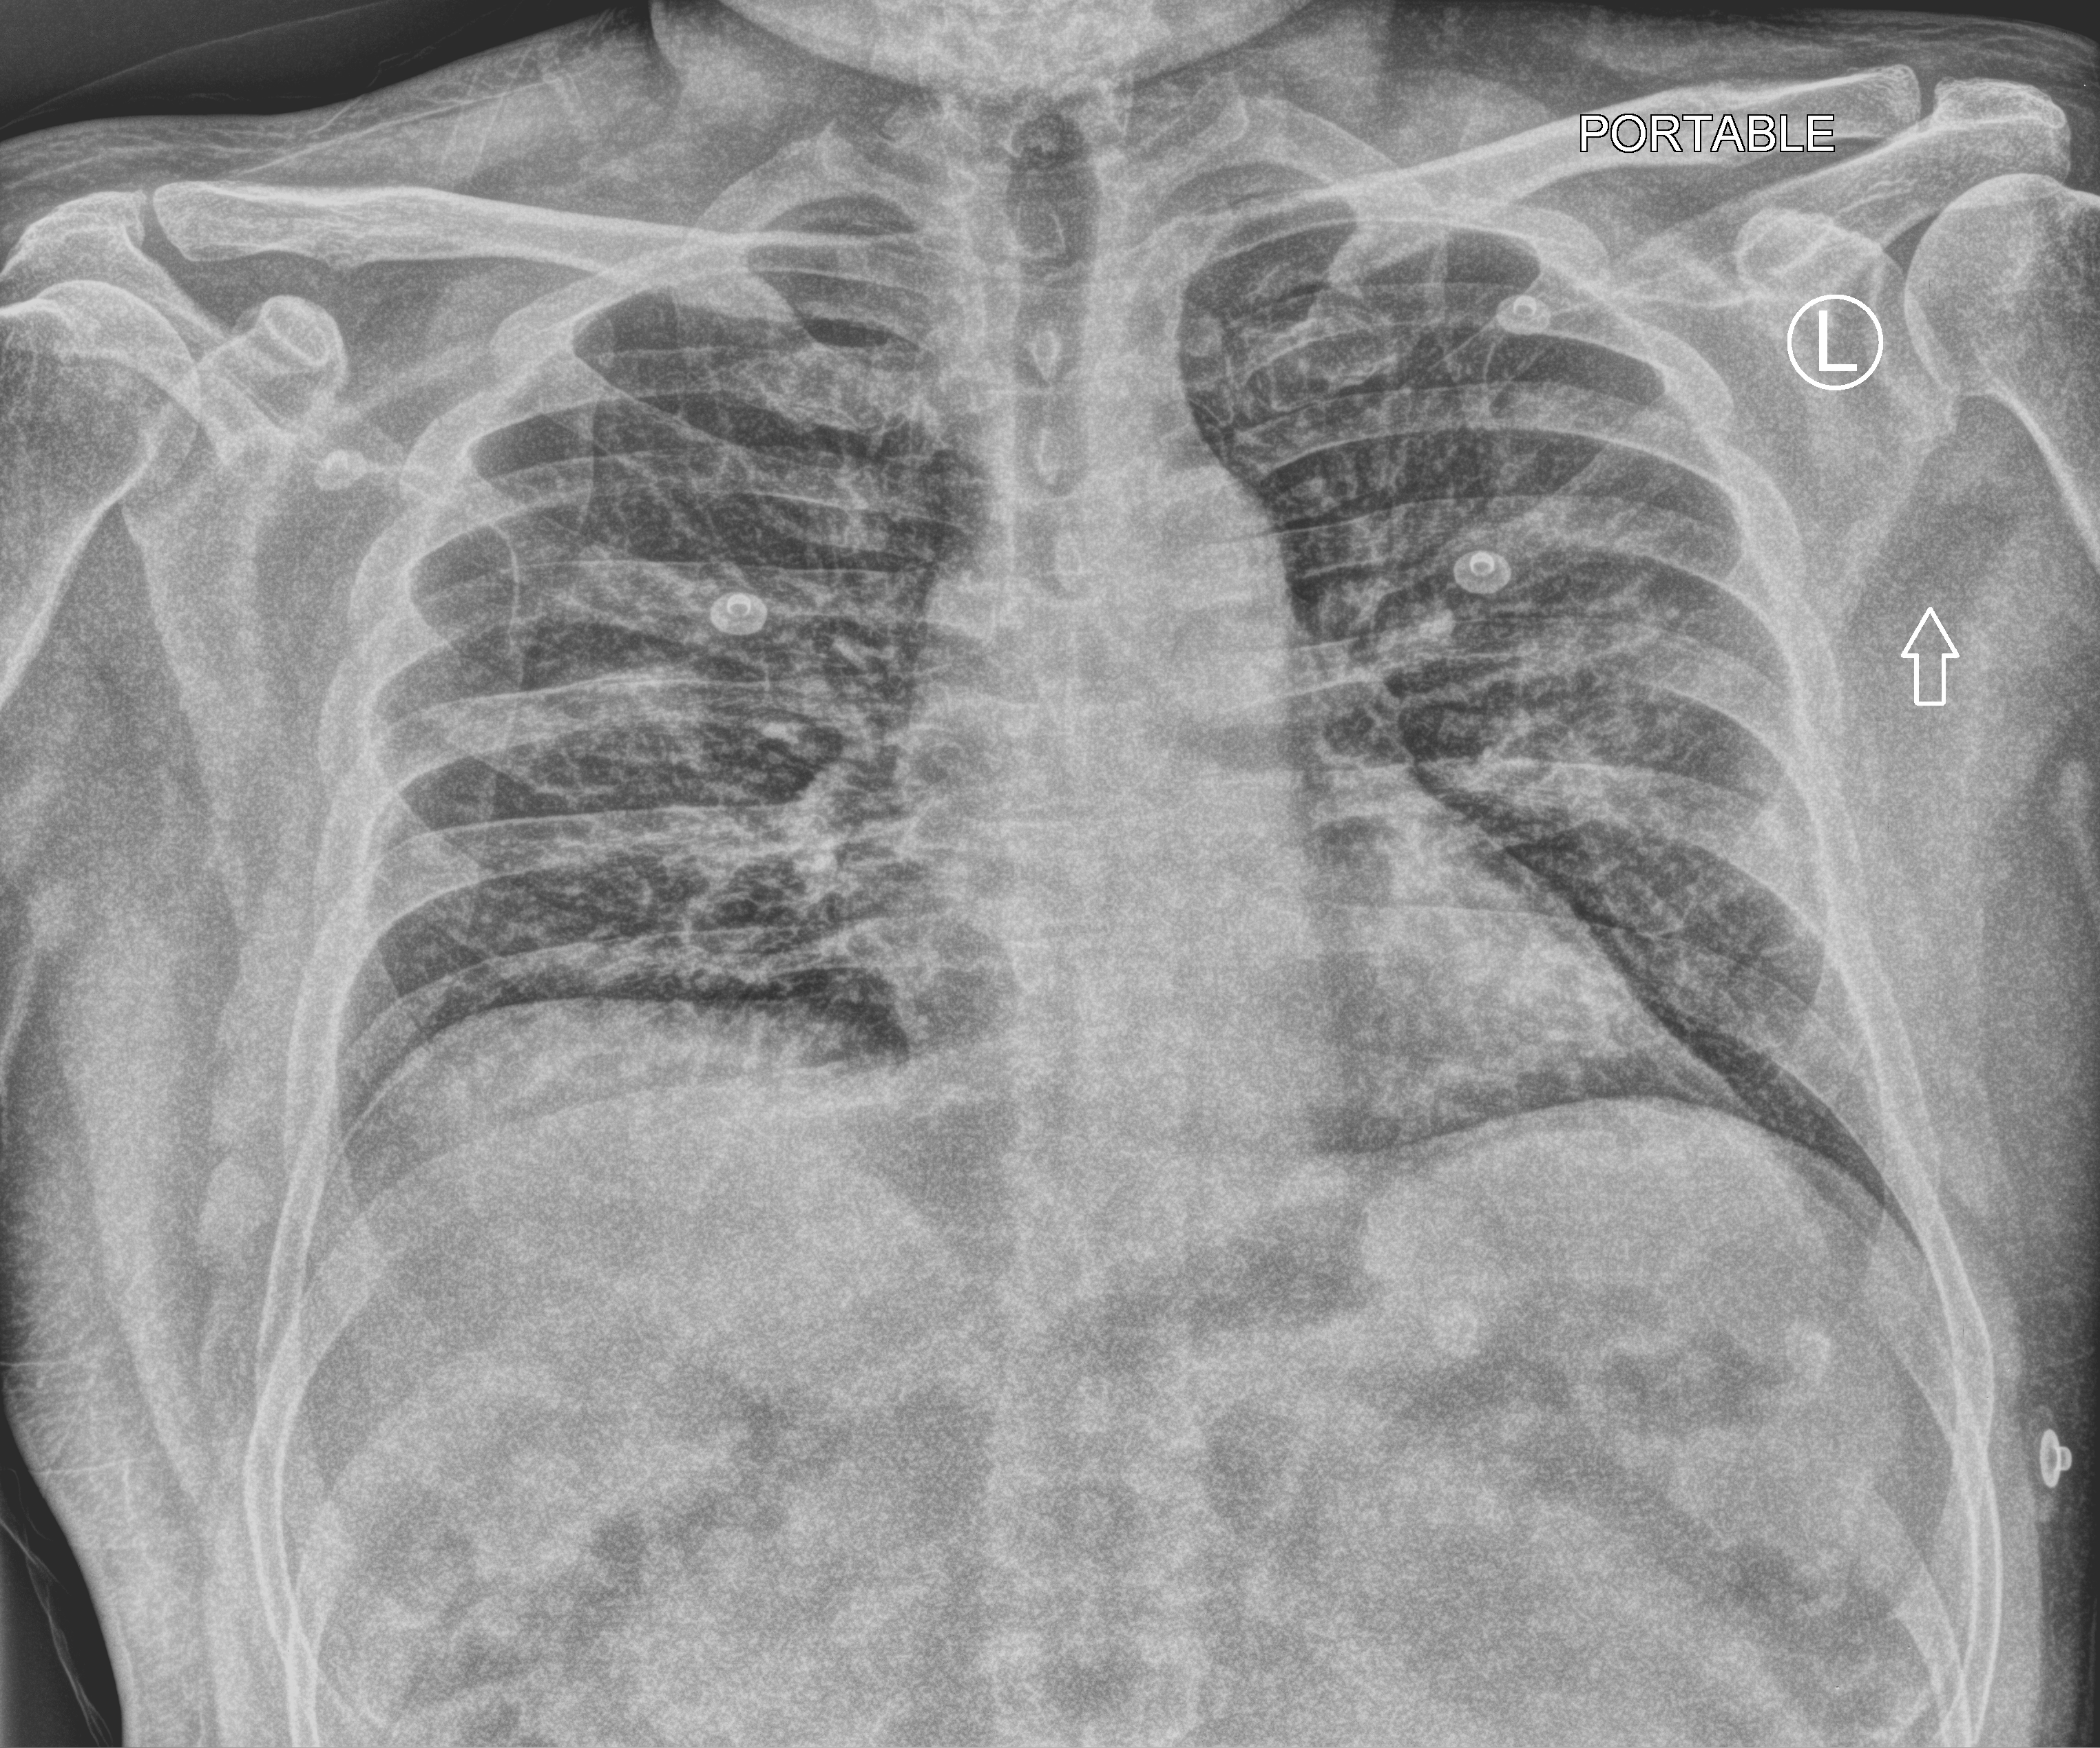
Bedside chest radiograph (computed radiography), anteroposterior (AP) projection. Patient hospitalised with COVID-19; male, aged 18–59 years.
From the hospital-stay record, not from the radiograph (when in the stay this image was taken is not recorded):
- length of hospital stay: 5 days
- mechanically ventilated during this hospital stay: no
- diabetes (admission record): no